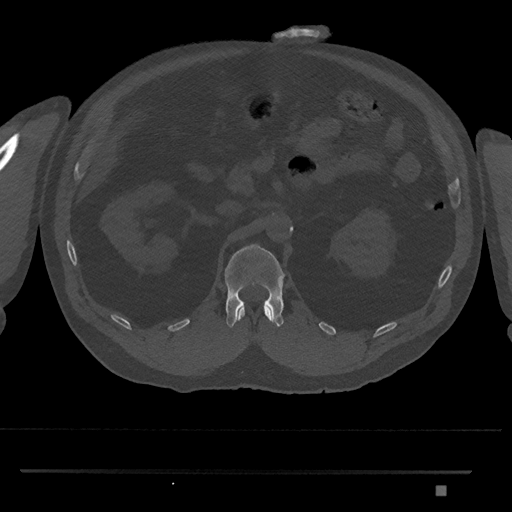
CT including the spine, one axial slice; slice 841 of 1134 in the series (ordered by position); reconstruction kernel Br40s/3; 120 kVp; bone window (W 1800 / L 400 HU); 0.5 mm slice thickness; 512 × 512 image matrix, field of view 429 × 429 mm. Patient: male, 65 years. Case-level facts recorded for this patient, not image findings: primary cancer: prostate.
Outlined on this slice (semi-automatically segmented with operator editing):
- L1 vertebra: box from (x=225, y=244) to (x=285, y=328) px
- T12 vertebra: (x=236, y=306)–(x=272, y=321)